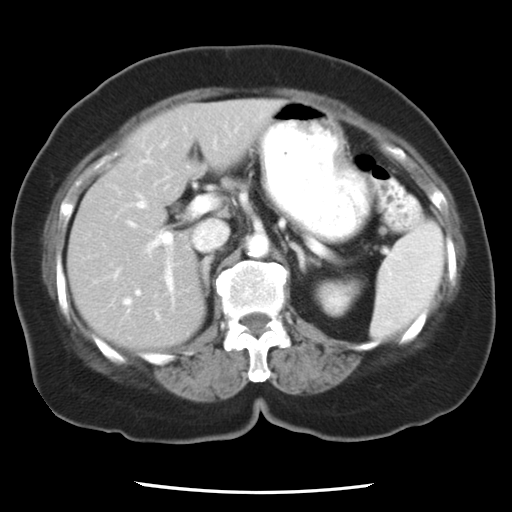
Contrast-enhanced abdominal CT, one axial slice; reconstruction kernel STANDARD; 120 kVp; soft-tissue window (W 400 / L 40 HU); 7.5 mm slice thickness; 512 × 512 image matrix, field of view 312 × 312 mm. Female patient, age 71 years. From the clinical record (not read from this slice): diagnosis: colorectal cancer liver metastases, imaged before liver resection; multiple liver metastases: no; largest metastasis: 4.3 cm.
Structures marked on this image (outlined manually by an expert reader):
- hepatic veins: bounding box [x1, y1, x2, y2] px = [124, 187, 195, 305]
- liver: [68, 100, 281, 349]
- planned liver remnant (the part of the liver to remain after resection): [68, 111, 205, 349]
- portal vein (with intrahepatic branches): [113, 223, 177, 305]